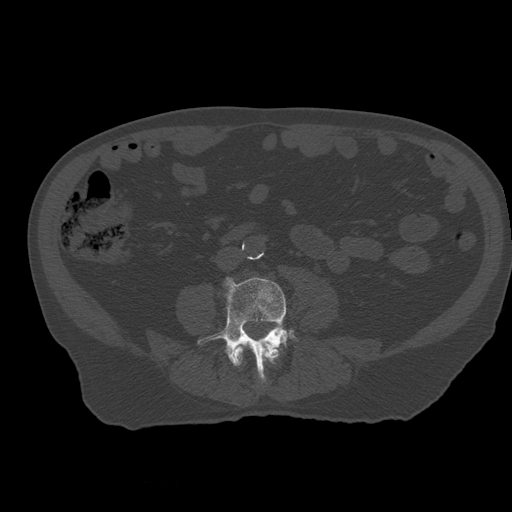
CT including the spine, one axial slice; slice 168 of 399 in the series (ordered by position); reconstruction kernel STANDARD; bone window (W 1800 / L 400 HU); 1.25 mm slice thickness; 512 × 512 image matrix. Patient age 73 years. Case-level facts recorded for this patient, not image findings: primary cancer: prostate.
Annotated regions visible in this slice (semi-automatic segmentation, software-assisted and operator-edited):
- L3 vertebra: box from (x=235, y=342) to (x=280, y=365) px
- L4 vertebra: (x=198, y=277)–(x=298, y=380)